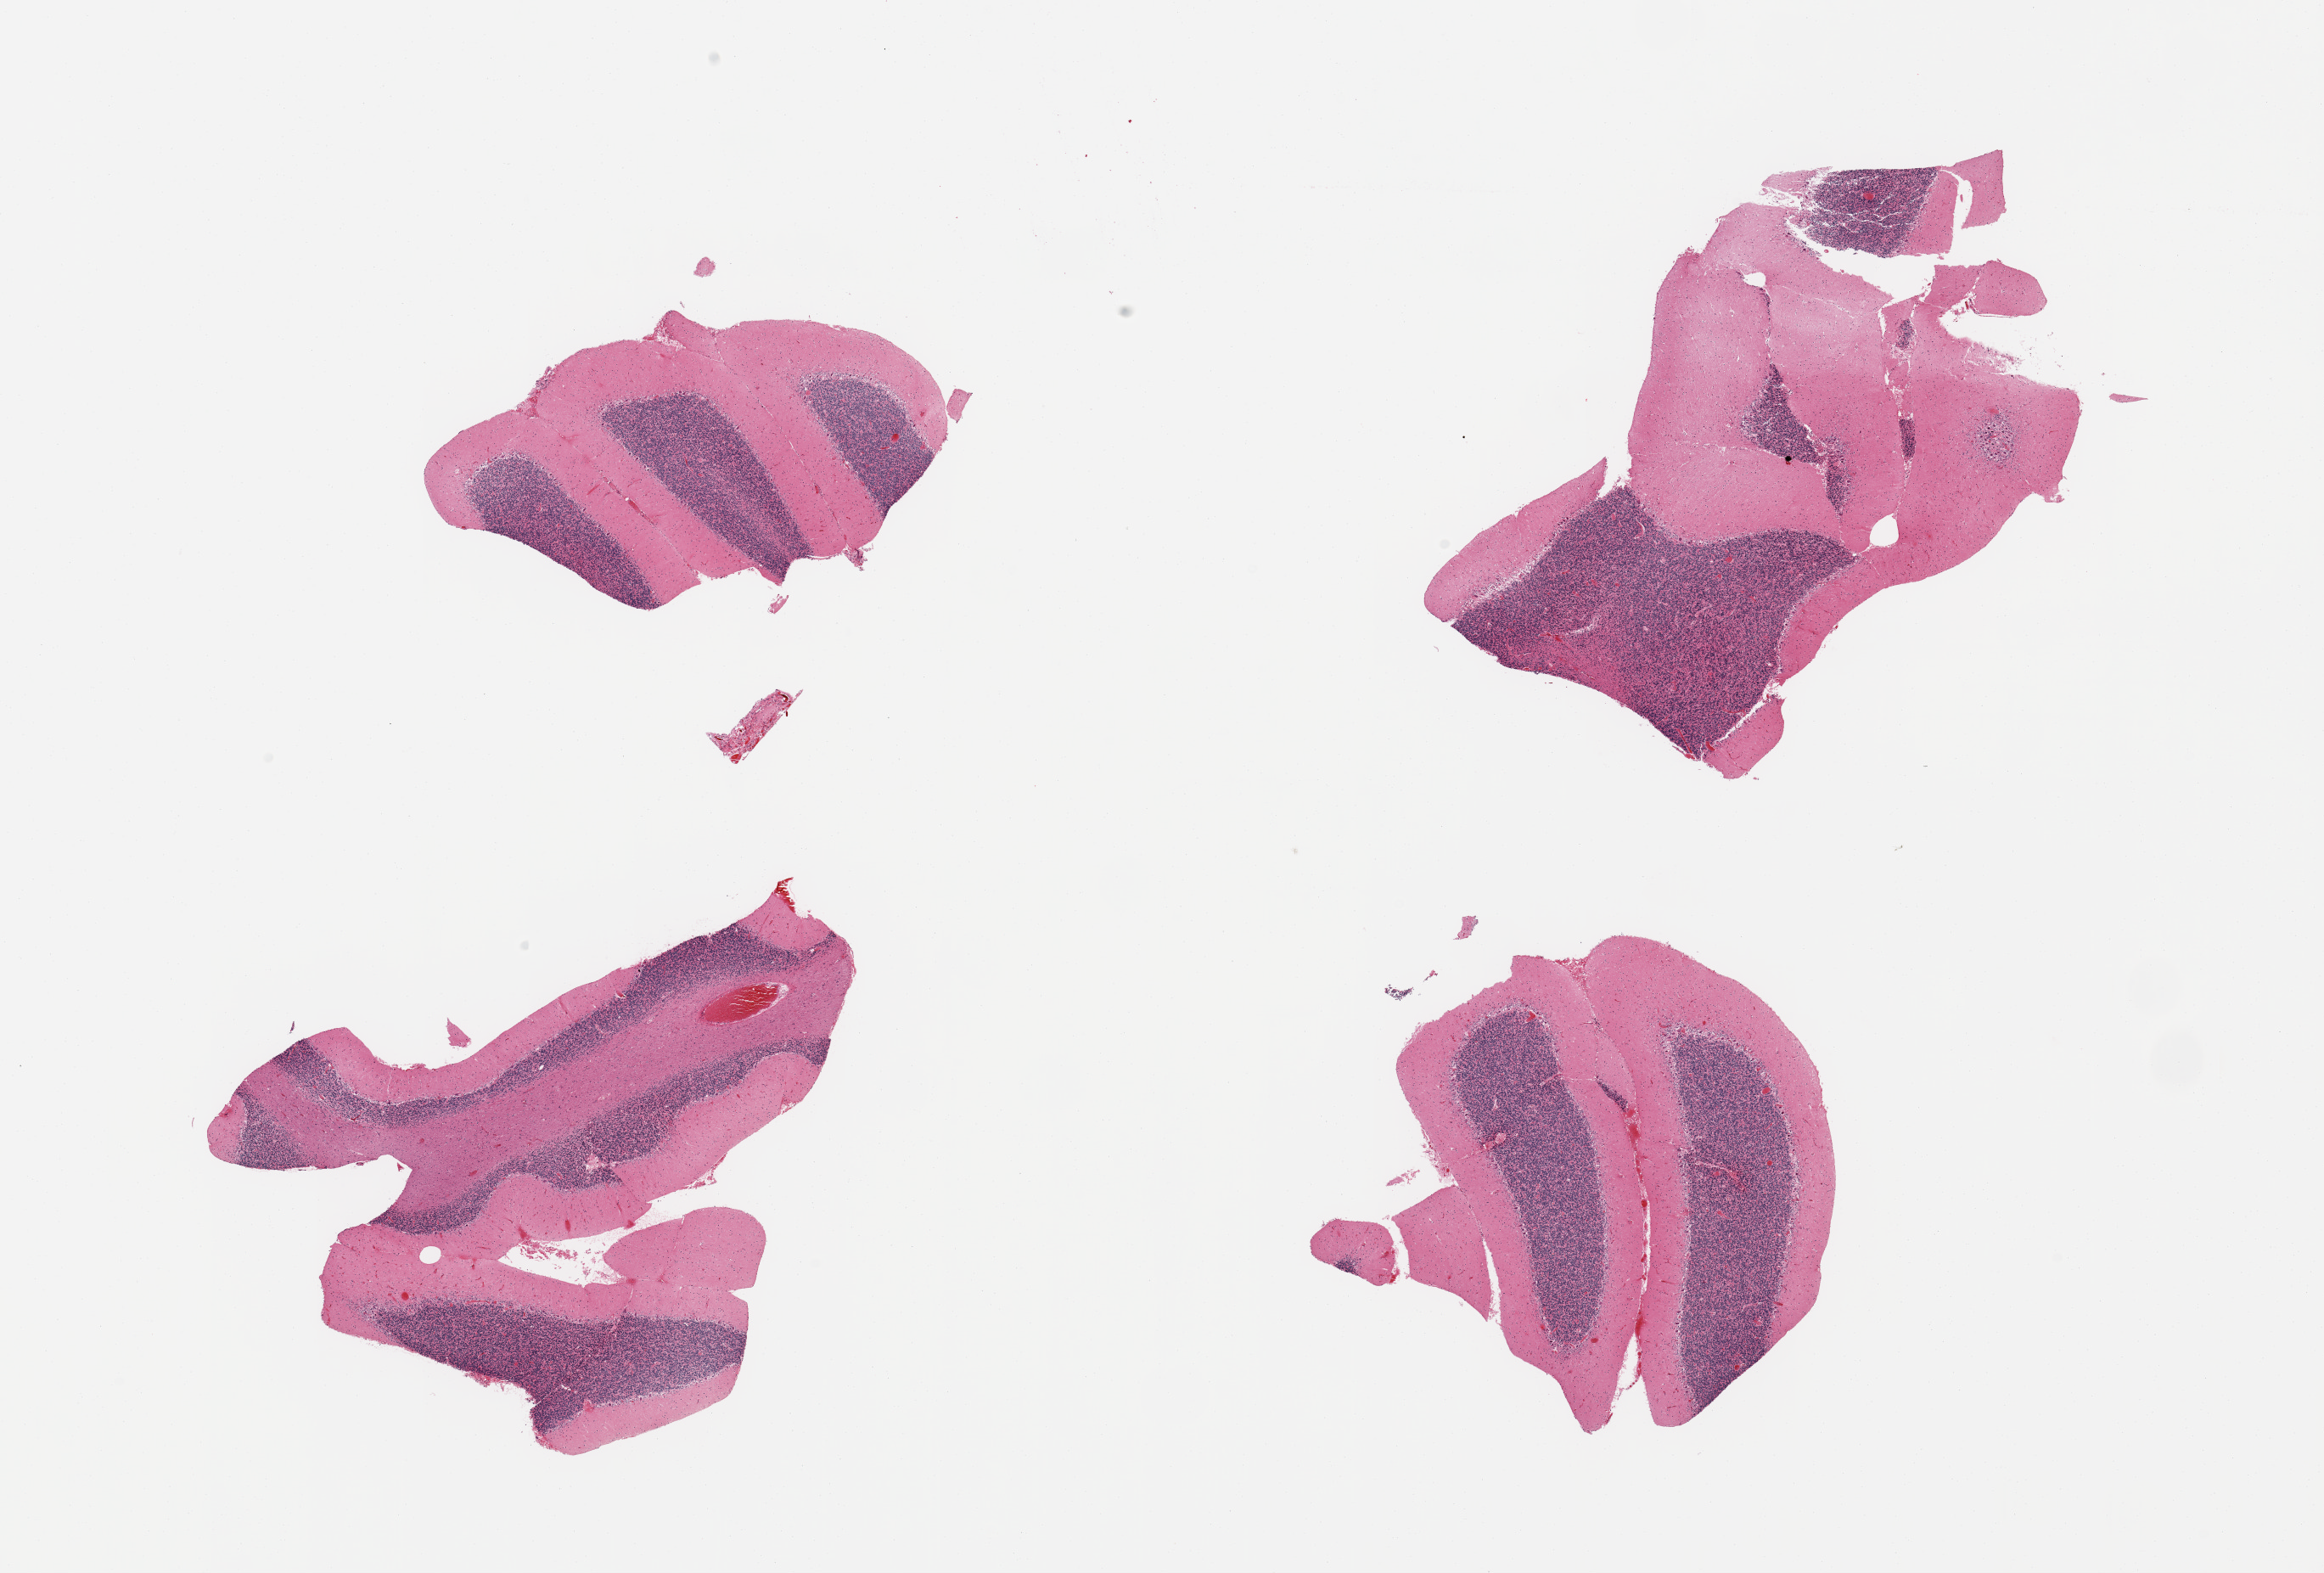
Whole-slide image, haematoxylin and eosin stain, a low-resolution overview of the entire scanned area, about 21.7 x 14.7 mm (slide scanned at 20x). PAXgene-fixed, paraffin-embedded tissue. Target tissue: cerebellum. Donor tissue sample. Donor sex: male.
* reviewer comment on this tissue sample: 4 pieces; mild to moderate autolysis; Purkinjie cells present